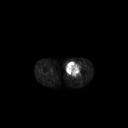
FDG PET of an extremity soft-tissue mass (from a PET/CT study), one axial slice. 3.27 mm slice thickness. 128 × 128 image matrix, field of view 700 × 700 mm. Male patient, age 63 years. From the clinical record (not read from this slice): histological type: pleiomorphic liposarcoma; grade: high; site of the primary tumour: left thigh.
Outlined on this slice (expert contour drawn on MRI and transferred to this co-registered scan by the dataset authors):
- gross tumour volume including surrounding oedema: bounding box <66,61,81,76> (left, top, right, bottom; pixels)
- gross tumour volume (mass): <66,62,80,75>